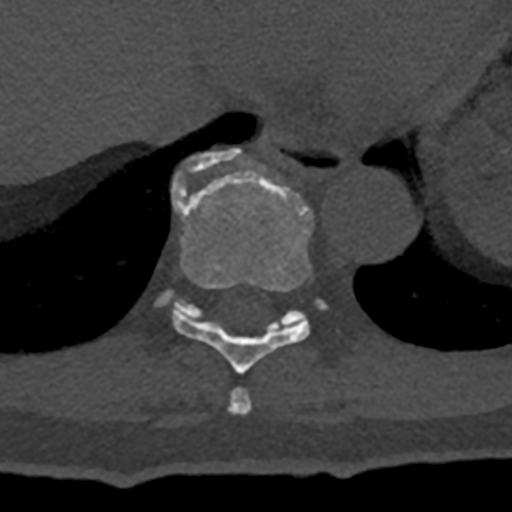
CT including the spine, one axial slice. Slice 642 of 797 in the series (ordered by position). Reconstruction kernel Br40s/3. 120 kVp. Bone window (W 1800 / L 400 HU). 512 × 512 image matrix, field of view 160 × 160 mm. Patient: male, 74 years. From the clinical record (not read from this slice): primary cancer: renal.
Structures marked on this image (semi-automatically segmented with operator editing):
- T10 vertebra: box from (x=156, y=149) to (x=327, y=328) px
- T8 vertebra: (x=229, y=388)–(x=252, y=415)
- T9 vertebra: (x=172, y=172)–(x=314, y=373)